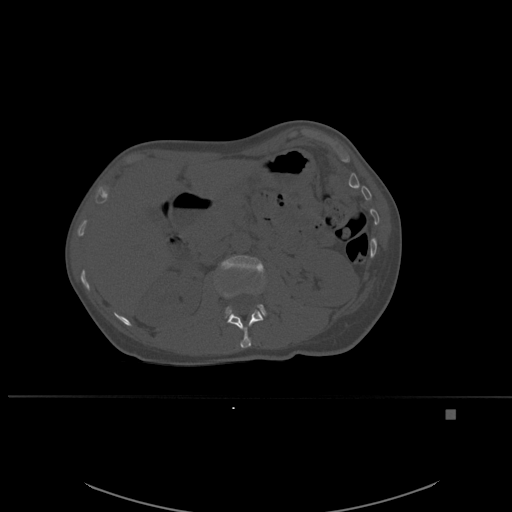
CT including the spine, one axial slice. Position 249 of 537 along the scan axis. Bone window (W 1800 / L 400 HU). 1.5 mm slice thickness. 512 × 512 image matrix, field of view 440 × 440 mm. Patient: female, 45 years. From the clinical record (not read from this slice): primary cancer: lung.
Outlined on this slice (semi-automatic segmentation, software-assisted and operator-edited):
- L1 vertebra: bounding box (x1, y1, x2, y2) in pixels: (216, 280, 264, 349)
- L2 vertebra: (221, 255, 266, 318)